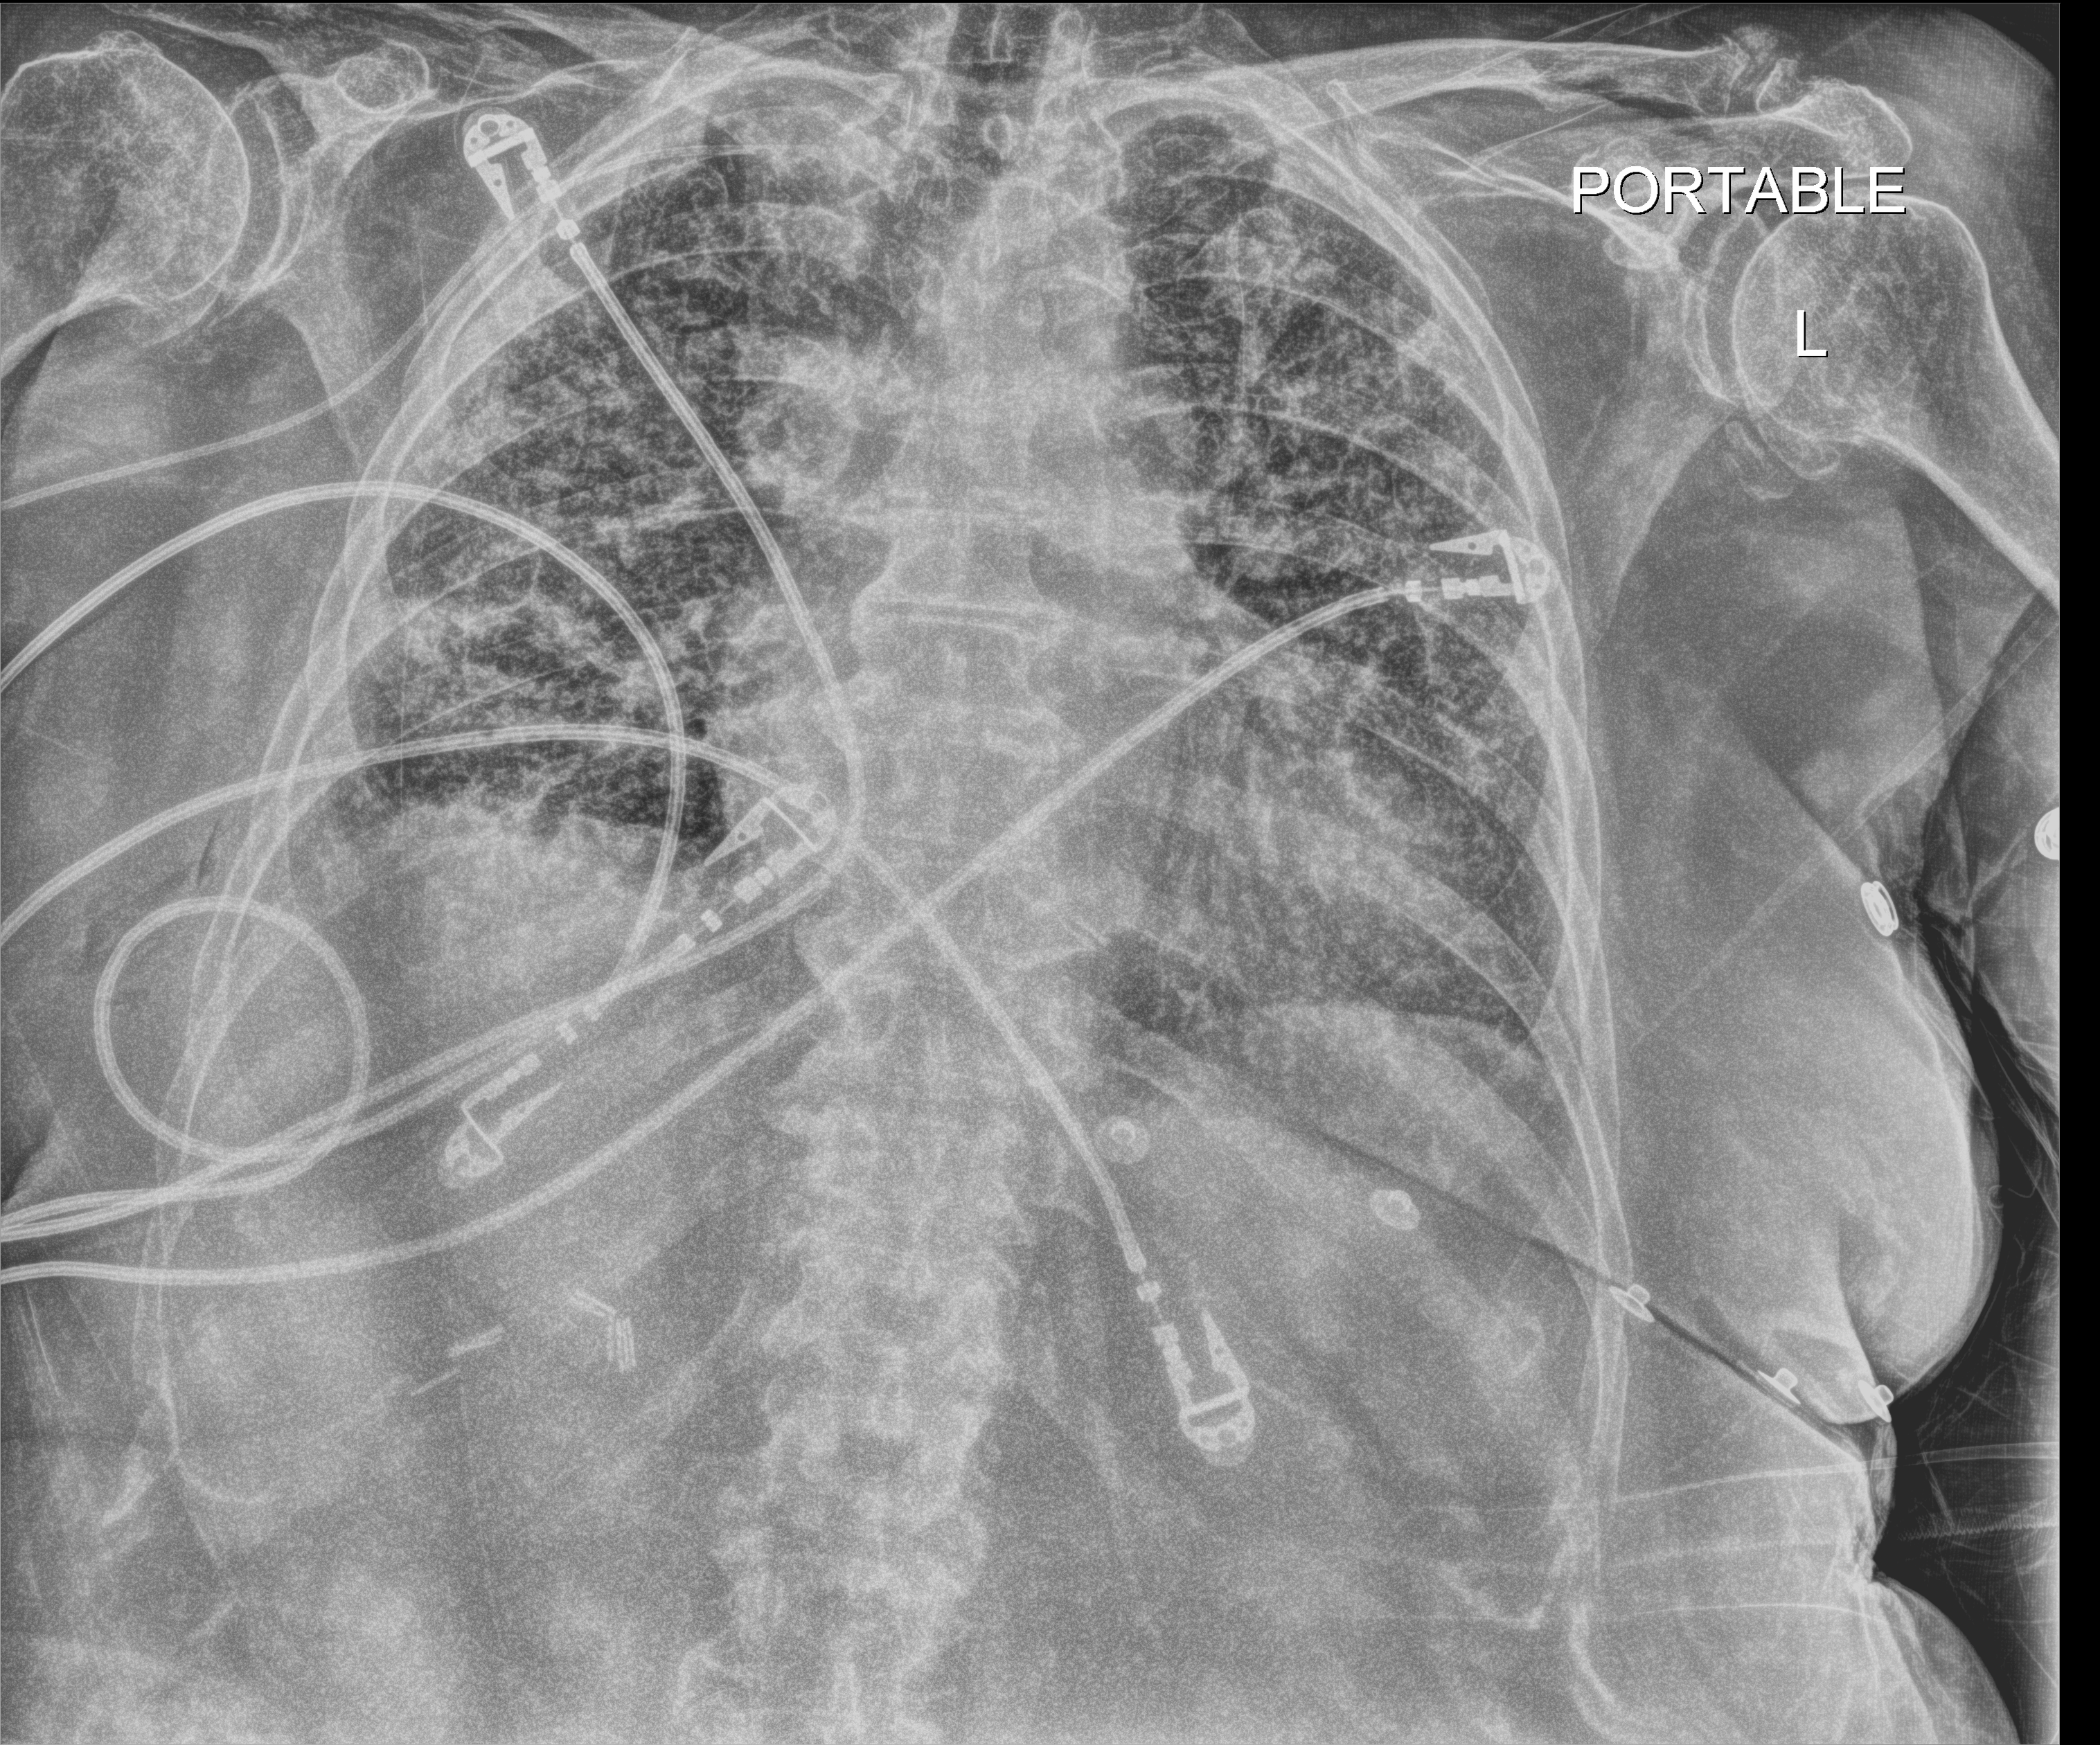
Chest X-ray (portable), anteroposterior (AP) projection. Patient hospitalised with COVID-19; female, aged 75–90 years.
Admission-level facts for this patient (not findings on this image; timing relative to this image not recorded): mechanically ventilated during this hospital stay: yes; length of hospital stay: 56 days.